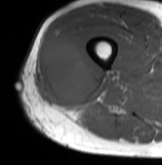
MRI of an extremity soft-tissue mass, one axial slice. Slice 33 of 61 in the series (ordered by position). MR volume resampled by the dataset authors to the PET/CT grid (not the native acquisition matrix). 3.27 mm slice thickness. 162 × 165 image matrix, field of view 158 × 161 mm. Male patient. From the clinical record (not read from this slice): histological type: poorly differentiated synovial sarcoma; grade: high; site of the primary tumour: right buttock.
Annotated regions visible in this slice (expert contour drawn on MRI and transferred to this co-registered scan by the dataset authors):
- gross tumour volume including surrounding oedema: box from (x=34, y=34) to (x=95, y=105) px
- gross tumour volume (mass): (x=43, y=38)–(x=95, y=105)